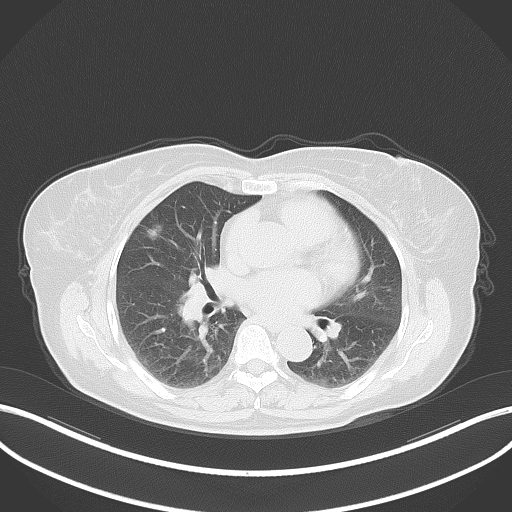
Chest CT, one axial slice. Slice 34 of 64 in the series (ordered by position). Reconstruction kernel B70f. Lung window (W 1500 / L -600 HU). 512 × 512 image matrix, field of view 400 × 400 mm. Patient: female, 55 years. From the clinical record (not read from this slice): clinical TNM (as recorded): T1b N0 M0; histopathological grade: G2.
Outlined on this slice (rectangle marked by the reading radiologist):
- lung tumour (recorded histology: adenocarcinoma): bounding box <140,218,165,244> (left, top, right, bottom; pixels)